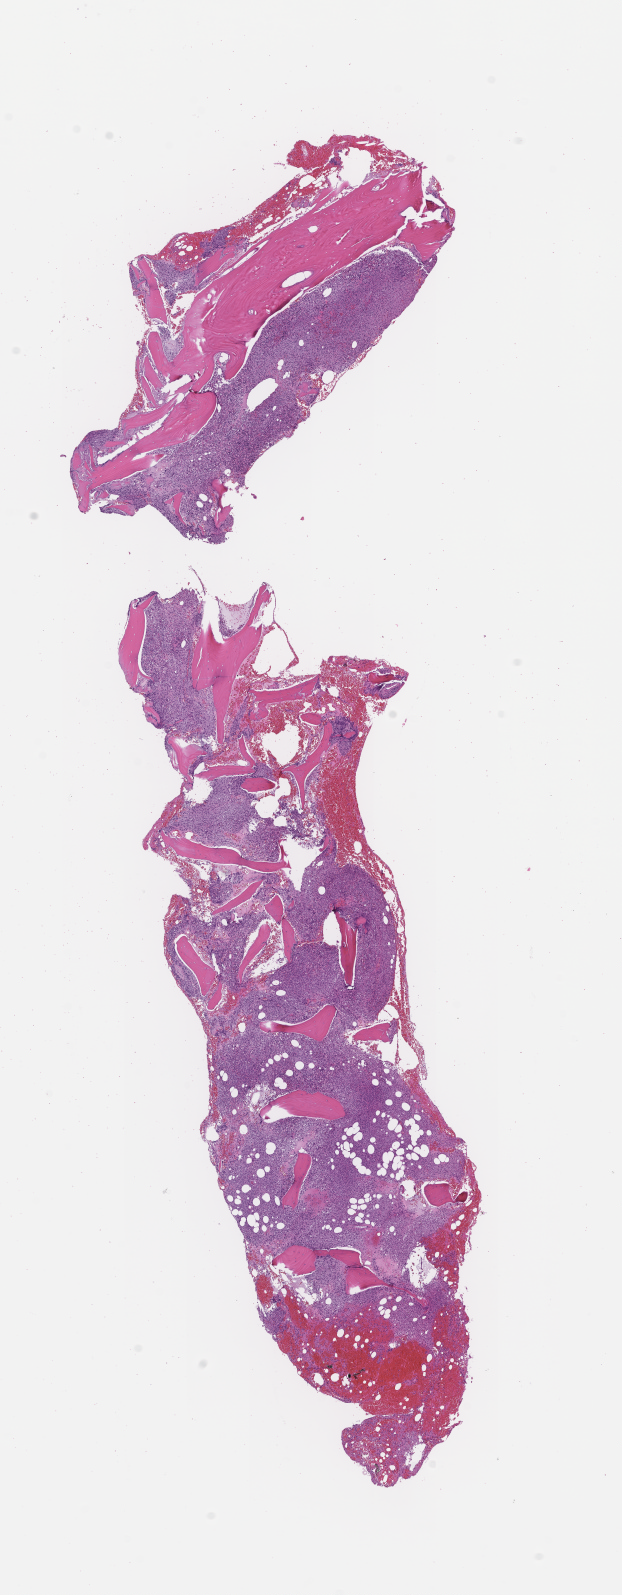
Whole-slide image, hematoxylin and eosin (H&E) stain — whole scanned area (about 5.0 x 12.9 mm) shown as a low-resolution overview, formalin-fixed paraffin-embedded section, tissue site: bone marrow. Female patient.
This section: primary tumour tissue. Diagnosis: Plasma Cell Myeloma.